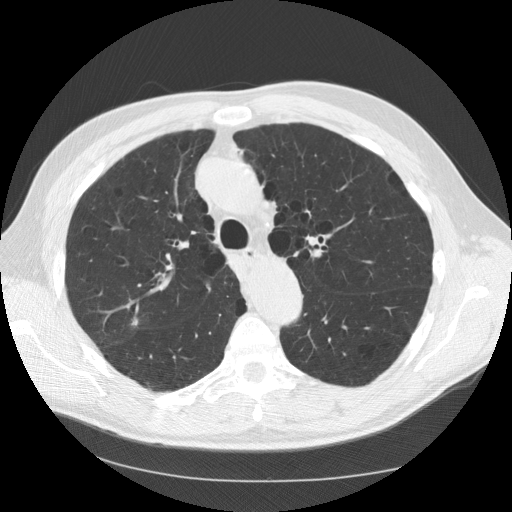
Low-dose screening chest CT, one axial slice. Slice 90 of 133 in the series (ordered by position). 120 kVp. Lung window (W 1500 / L -600 HU). 2.5 mm slice thickness. 512 × 512 image matrix, field of view 377 × 377 mm.
Outlined on this slice (outlined manually by an expert reader):
- lesion 1 (tumor, upper lobe of right lung): bounding box [x1, y1, x2, y2] px = [131, 317, 138, 326]